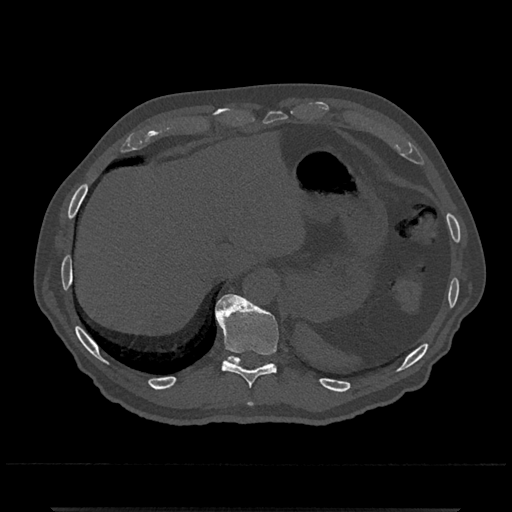
CT including the spine, one axial slice. Position 543 of 797 along the scan axis. Reconstruction kernel Br40s/3. 120 kVp. Bone window (W 1800 / L 400 HU). 512 × 512 image matrix, field of view 393 × 393 mm. Patient: male, 67 years. Case-level facts recorded for this patient, not image findings: primary cancer: prostate.
Outlined on this slice (semi-automatic segmentation, software-assisted and operator-edited):
- T10 vertebra: bounding box [x1, y1, x2, y2] px = [215, 294, 279, 388]
- T11 vertebra: [225, 356, 271, 366]
- T9 vertebra: [249, 402, 252, 405]